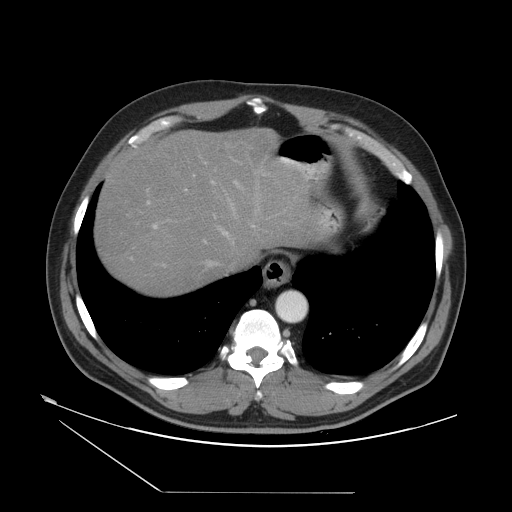
Contrast-enhanced abdominal CT, one axial slice; position 43 of 55 along the scan axis; reconstruction kernel STANDARD; 120 kVp; soft-tissue window (W 400 / L 40 HU); 5 mm slice thickness; 512 × 512 image matrix. Male patient, age 59 years. Case-level facts recorded for this patient, not image findings: diagnosis: colorectal cancer liver metastases, imaged before liver resection; multiple liver metastases: yes.
Annotated regions visible in this slice (outlined manually by an expert reader):
- hepatic veins: bounding box [x1, y1, x2, y2] px = [155, 171, 261, 267]
- liver: [97, 131, 308, 295]
- planned liver remnant (the part of the liver to remain after resection): [97, 155, 257, 295]
- portal vein (with intrahepatic branches): [130, 158, 268, 267]
- liver metastasis: [218, 144, 229, 155]